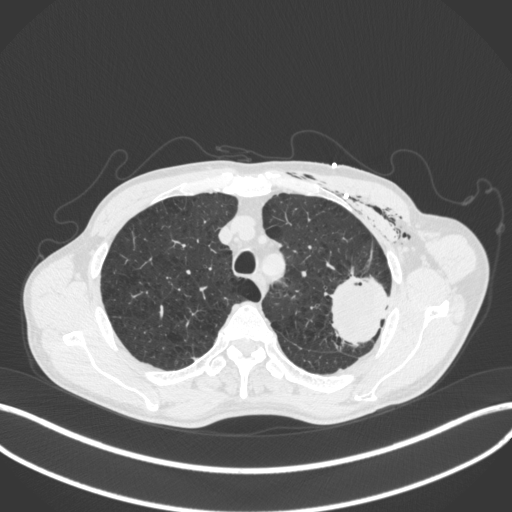
Chest CT, one axial slice. Slice 317 of 416 in the series (ordered by position). Reconstruction kernel B31f. Lung window (W 1500 / L -600 HU). 512 × 512 image matrix, field of view 400 × 400 mm. Patient: male, 58 years. Case-level facts recorded for this patient, not image findings: clinical TNM (as recorded): T3 N0 M0.
Annotated regions visible in this slice (bounding box drawn by a radiologist):
- lung tumour (recorded histology: adenocarcinoma): bounding box [x1, y1, x2, y2] px = [323, 271, 395, 349]